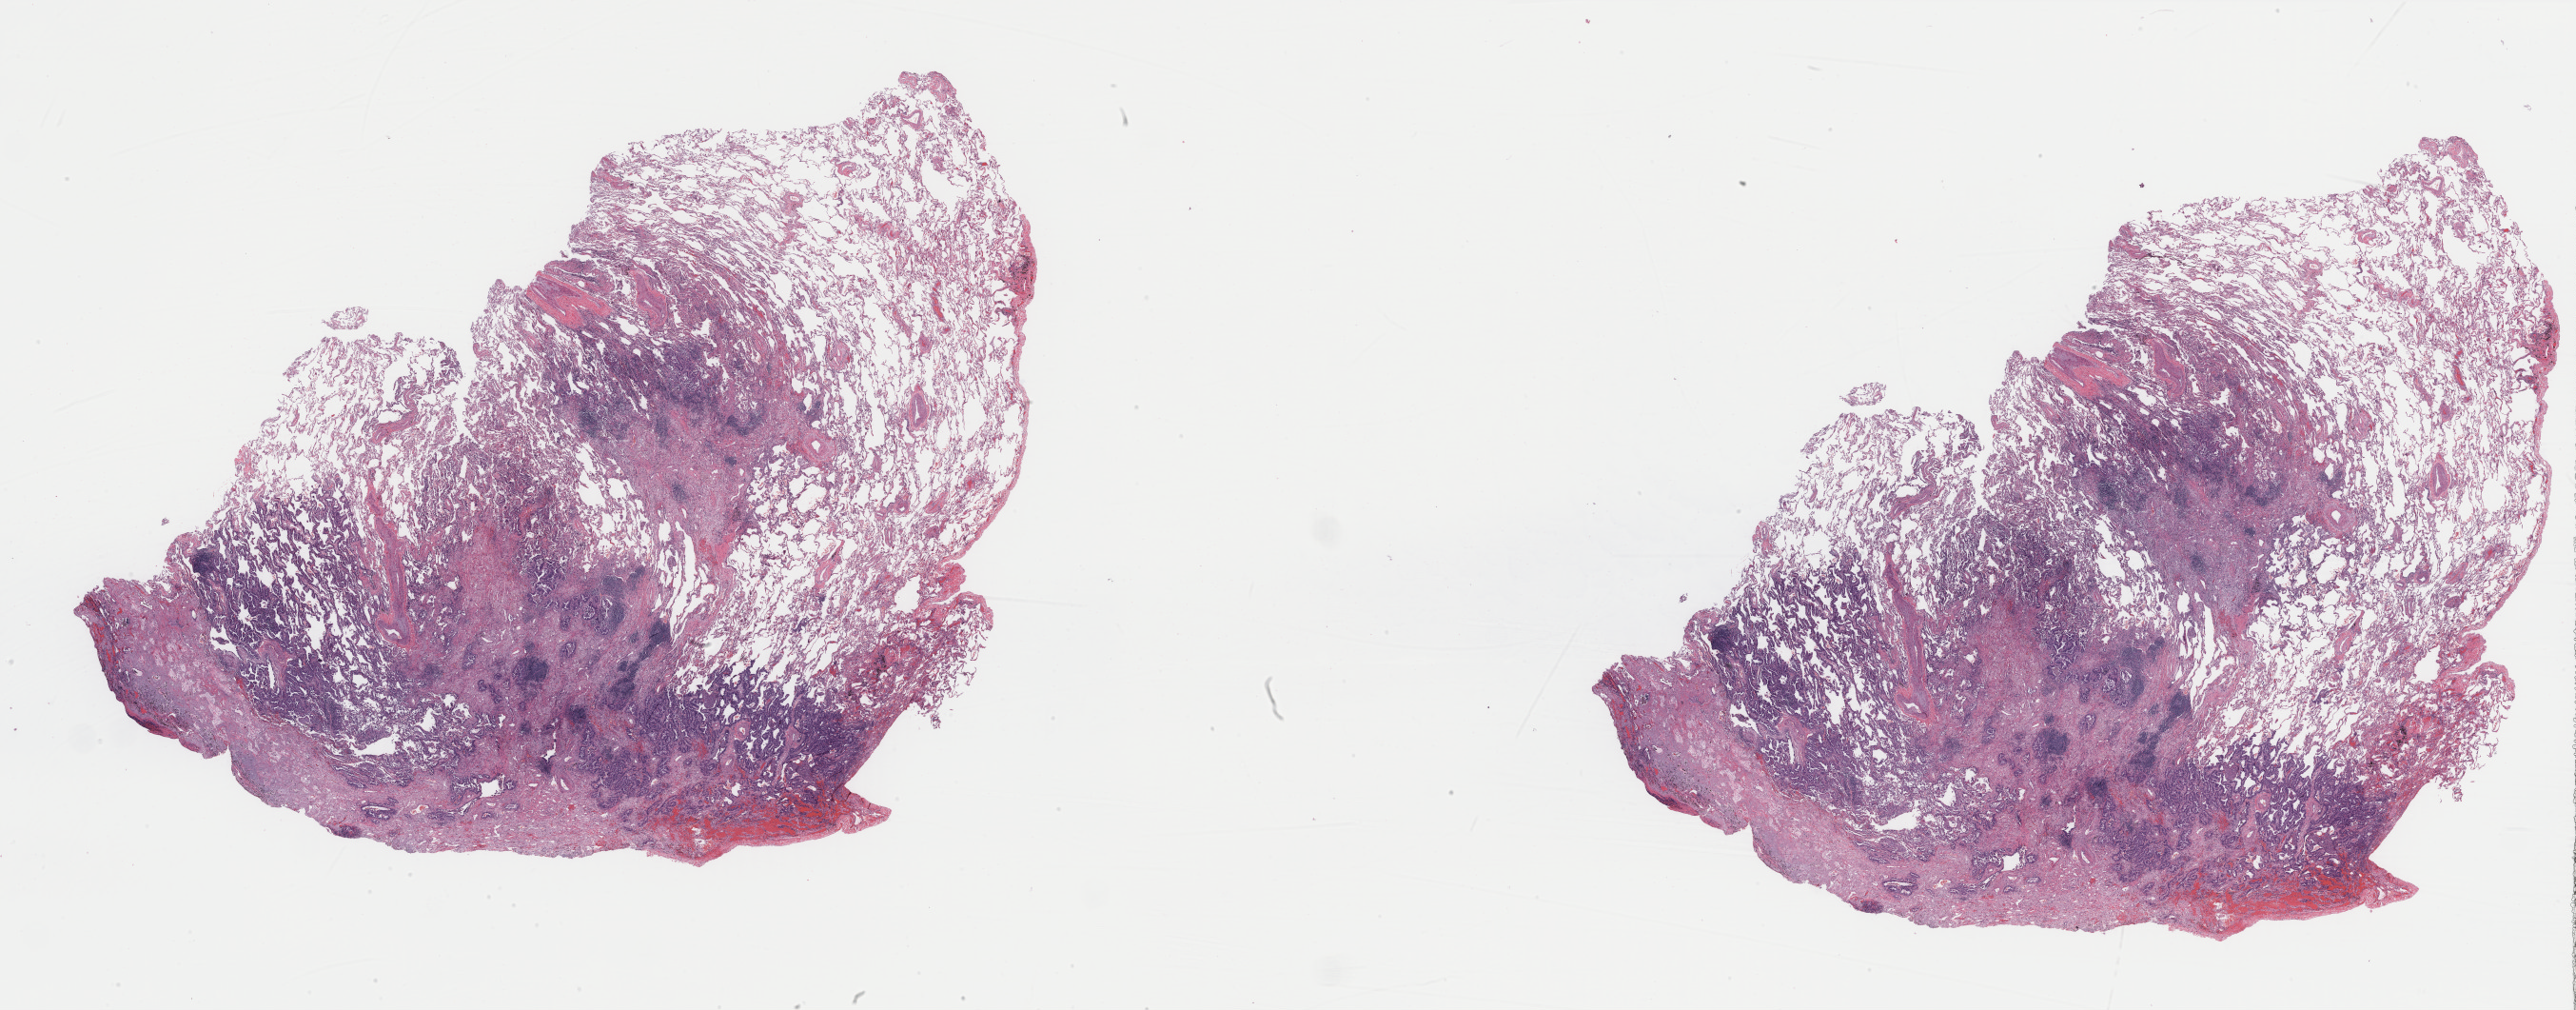
Hematoxylin and eosin (H&E) stained whole-slide image, low-resolution overview of the scanned area, about 43.0 x 16.8 mm. Formalin-fixed paraffin-embedded (FFPE) diagnostic section. Primary tumour sample from the lung. Male, age 72 years at initial diagnosis.
Diagnosis: Acinar cell carcinoma (upper lobe, lung). AJCC pathologic stage: IA (7th edition).